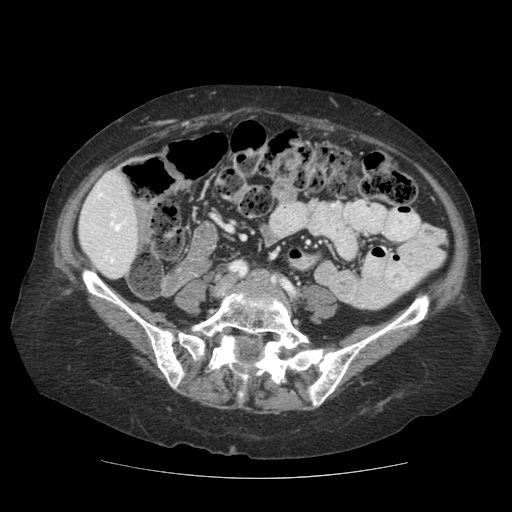
Contrast-enhanced abdominal CT (liver protocol), one axial slice. Position 23 of 111 along the scan axis. Reconstruction kernel STANDARD. 140 kVp. Soft-tissue window (W 400 / L 40 HU). 2.5 mm slice thickness. 512 × 512 image matrix. From the clinical record (not read from this slice): diagnosis: hepatocellular carcinoma (patient treated with transarterial chemoembolisation; whether this scan precedes or follows treatment is not stated here); TNM stage (as recorded): Stage-I.
Structures marked on this image (semi-automatically segmented with operator editing):
- liver parenchyma outside the tumour (the mass and vessels are separate outlines, so this box may not span the whole liver): bounding box (x1, y1, x2, y2) in pixels: (78, 170, 138, 278)
- liver vessels: (98, 187, 125, 263)